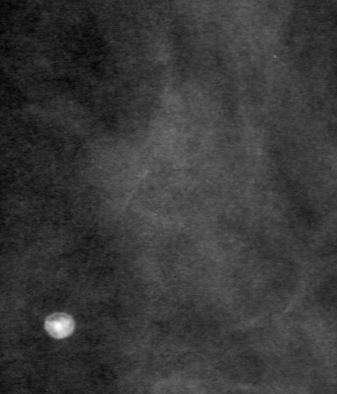
Region of interest cut from a scanned film mammogram (one marked finding); left breast; CC view; BI-RADS breast density category 1 (scale 1–4).
Marked abnormality: mass, shape lobulated, margins obscured; BI-RADS assessment category 0 (incomplete: needs additional imaging); pathology result (as recorded, not read from the image): benign.